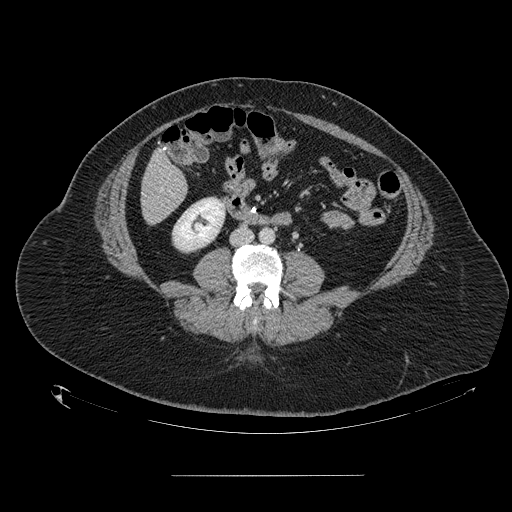
Contrast-enhanced abdominal CT, one axial slice; position 26 of 164 along the scan axis; 120 kVp; intravenous contrast given; soft-tissue window (W 400 / L 40 HU); 2.5 mm slice thickness; 512 × 512 image matrix, field of view 495 × 495 mm. Female patient, age 52 years. Case-level facts recorded for this patient, not image findings: diagnosis: colorectal cancer liver metastases, imaged before liver resection; multiple liver metastases: yes; largest metastasis: 3.5 cm; disease in both lobes: no.
Structures marked on this image (outlined manually by an expert reader):
- hepatic veins: bounding box <160,188,163,191> (left, top, right, bottom; pixels)
- liver: <142,152,187,224>